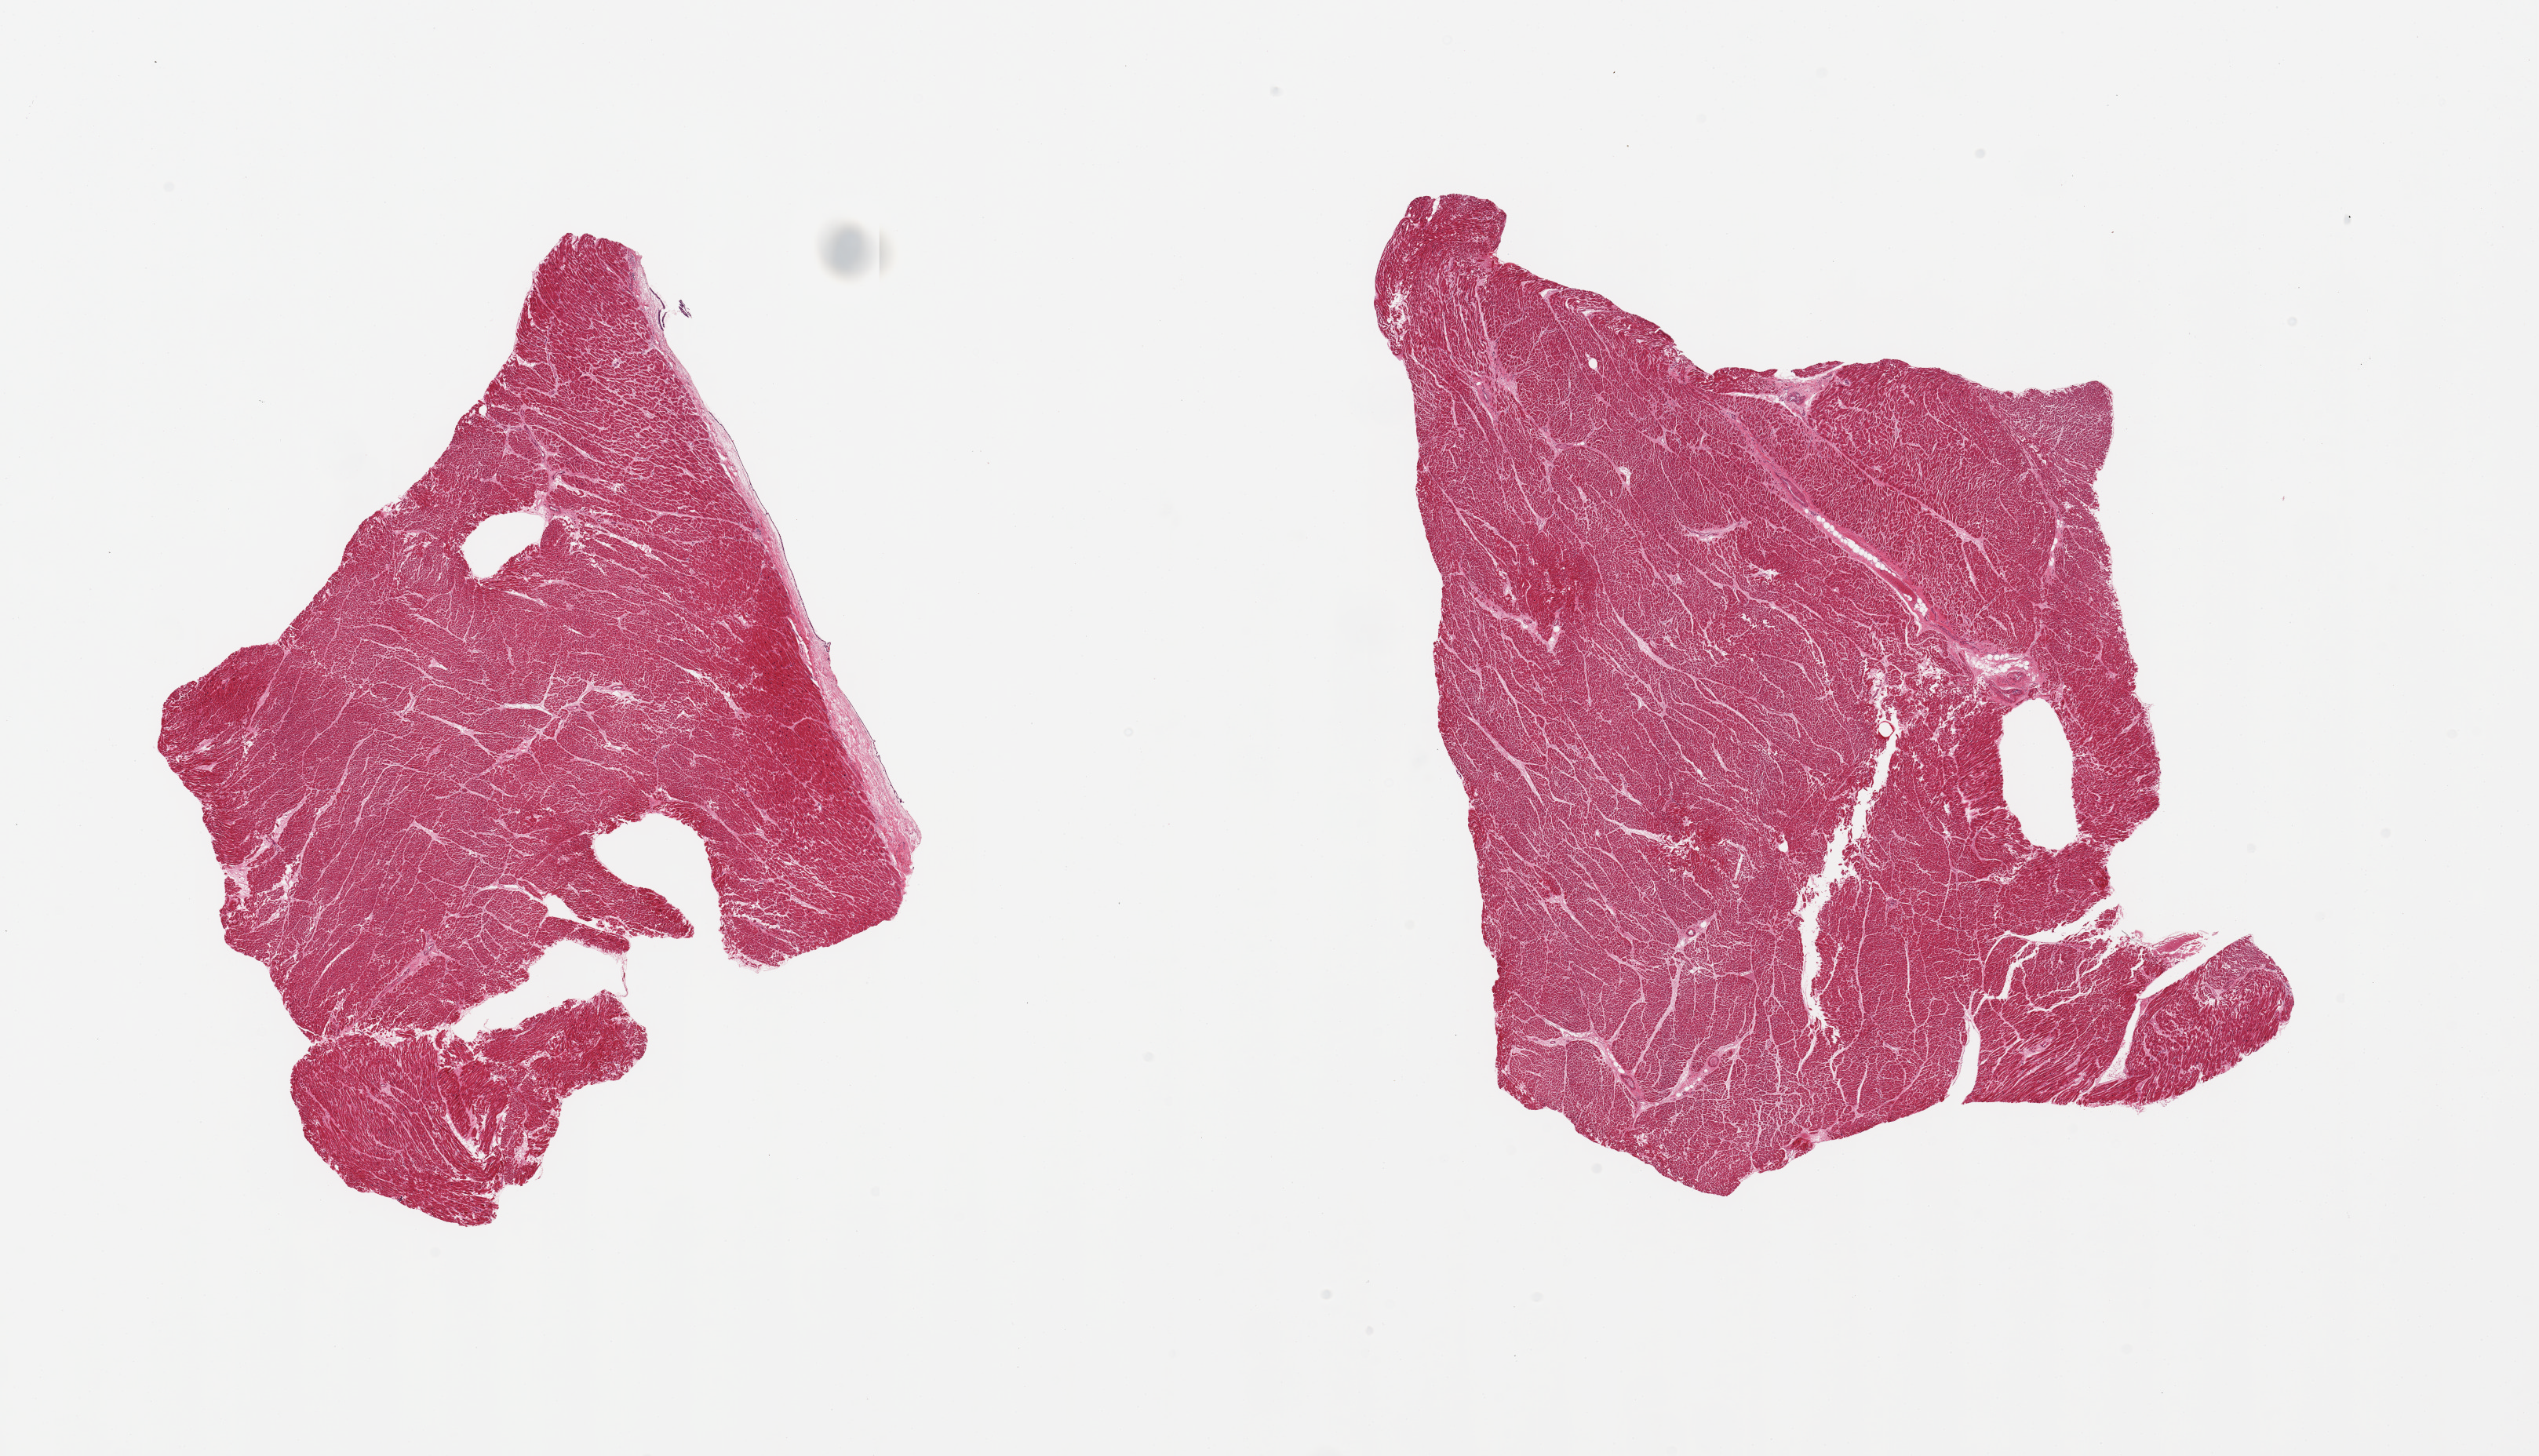
Digitized H&E-stained section — shown as a low-resolution overview of the whole scanned area (about 25.6 x 14.7 mm). PAXgene-fixed paraffin-embedded (PFPE) section. Section of heart (target tissue). Donor tissue sample. Male donor.
Reviewer comment on this tissue sample: 2 pieces.